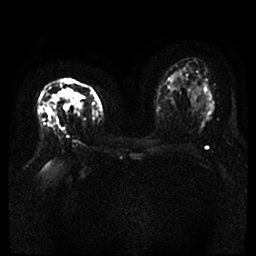
Breast MRI, one axial slice; position 19 of 46 along the scan axis; diffusion-weighted series; image 2 of 4 stored at this slice position (different b-values; order by instance number); 1.5 T; 4 mm slice thickness; 256 × 256 image matrix, field of view 360 × 360 mm. Female patient.
Structures marked on this image (manually delineated by an expert):
- tumour on diffusion-weighted imaging: bounding box <47,89,83,116> (left, top, right, bottom; pixels)